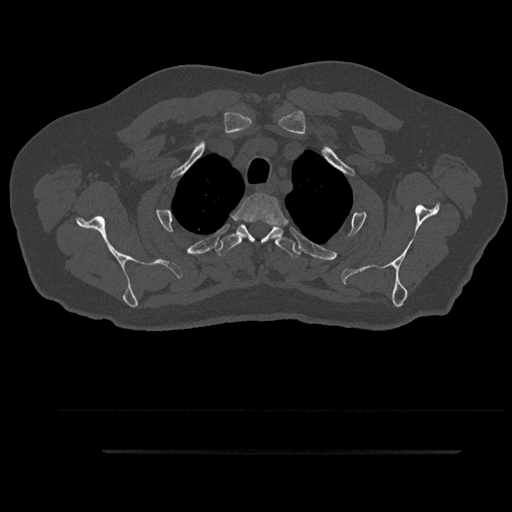
CT including the spine, one axial slice; slice 737 of 797 in the series (ordered by position); 120 kVp; bone window (W 1800 / L 400 HU); 0.5 mm slice thickness; 512 × 512 image matrix. Patient: male, 63 years. From the clinical record (not read from this slice): primary cancer: renal; vertebrae with lytic lesions (as recorded): T8.
Structures marked on this image (semi-automatic segmentation, software-assisted and operator-edited):
- T2 vertebra: bounding box (x1, y1, x2, y2) in pixels: (234, 193, 285, 244)
- T3 vertebra: (215, 223, 301, 258)